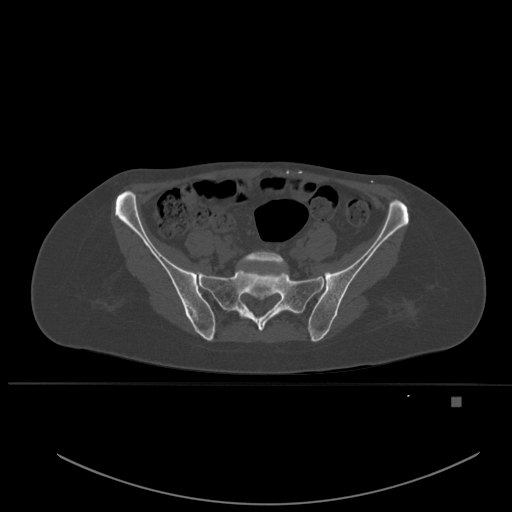
CT including the spine, one axial slice; slice 139 of 651 in the series (ordered by position); bone window (W 1800 / L 400 HU); 512 × 512 image matrix, field of view 443 × 443 mm. Female patient, age 49 years. Case-level facts recorded for this patient, not image findings: primary cancer: breast; vertebrae with lytic lesions (as recorded): L3, T12, L4.
Annotated regions visible in this slice (semi-automatically segmented with operator editing):
- L5 vertebra: bounding box [x1, y1, x2, y2] px = [239, 252, 286, 266]